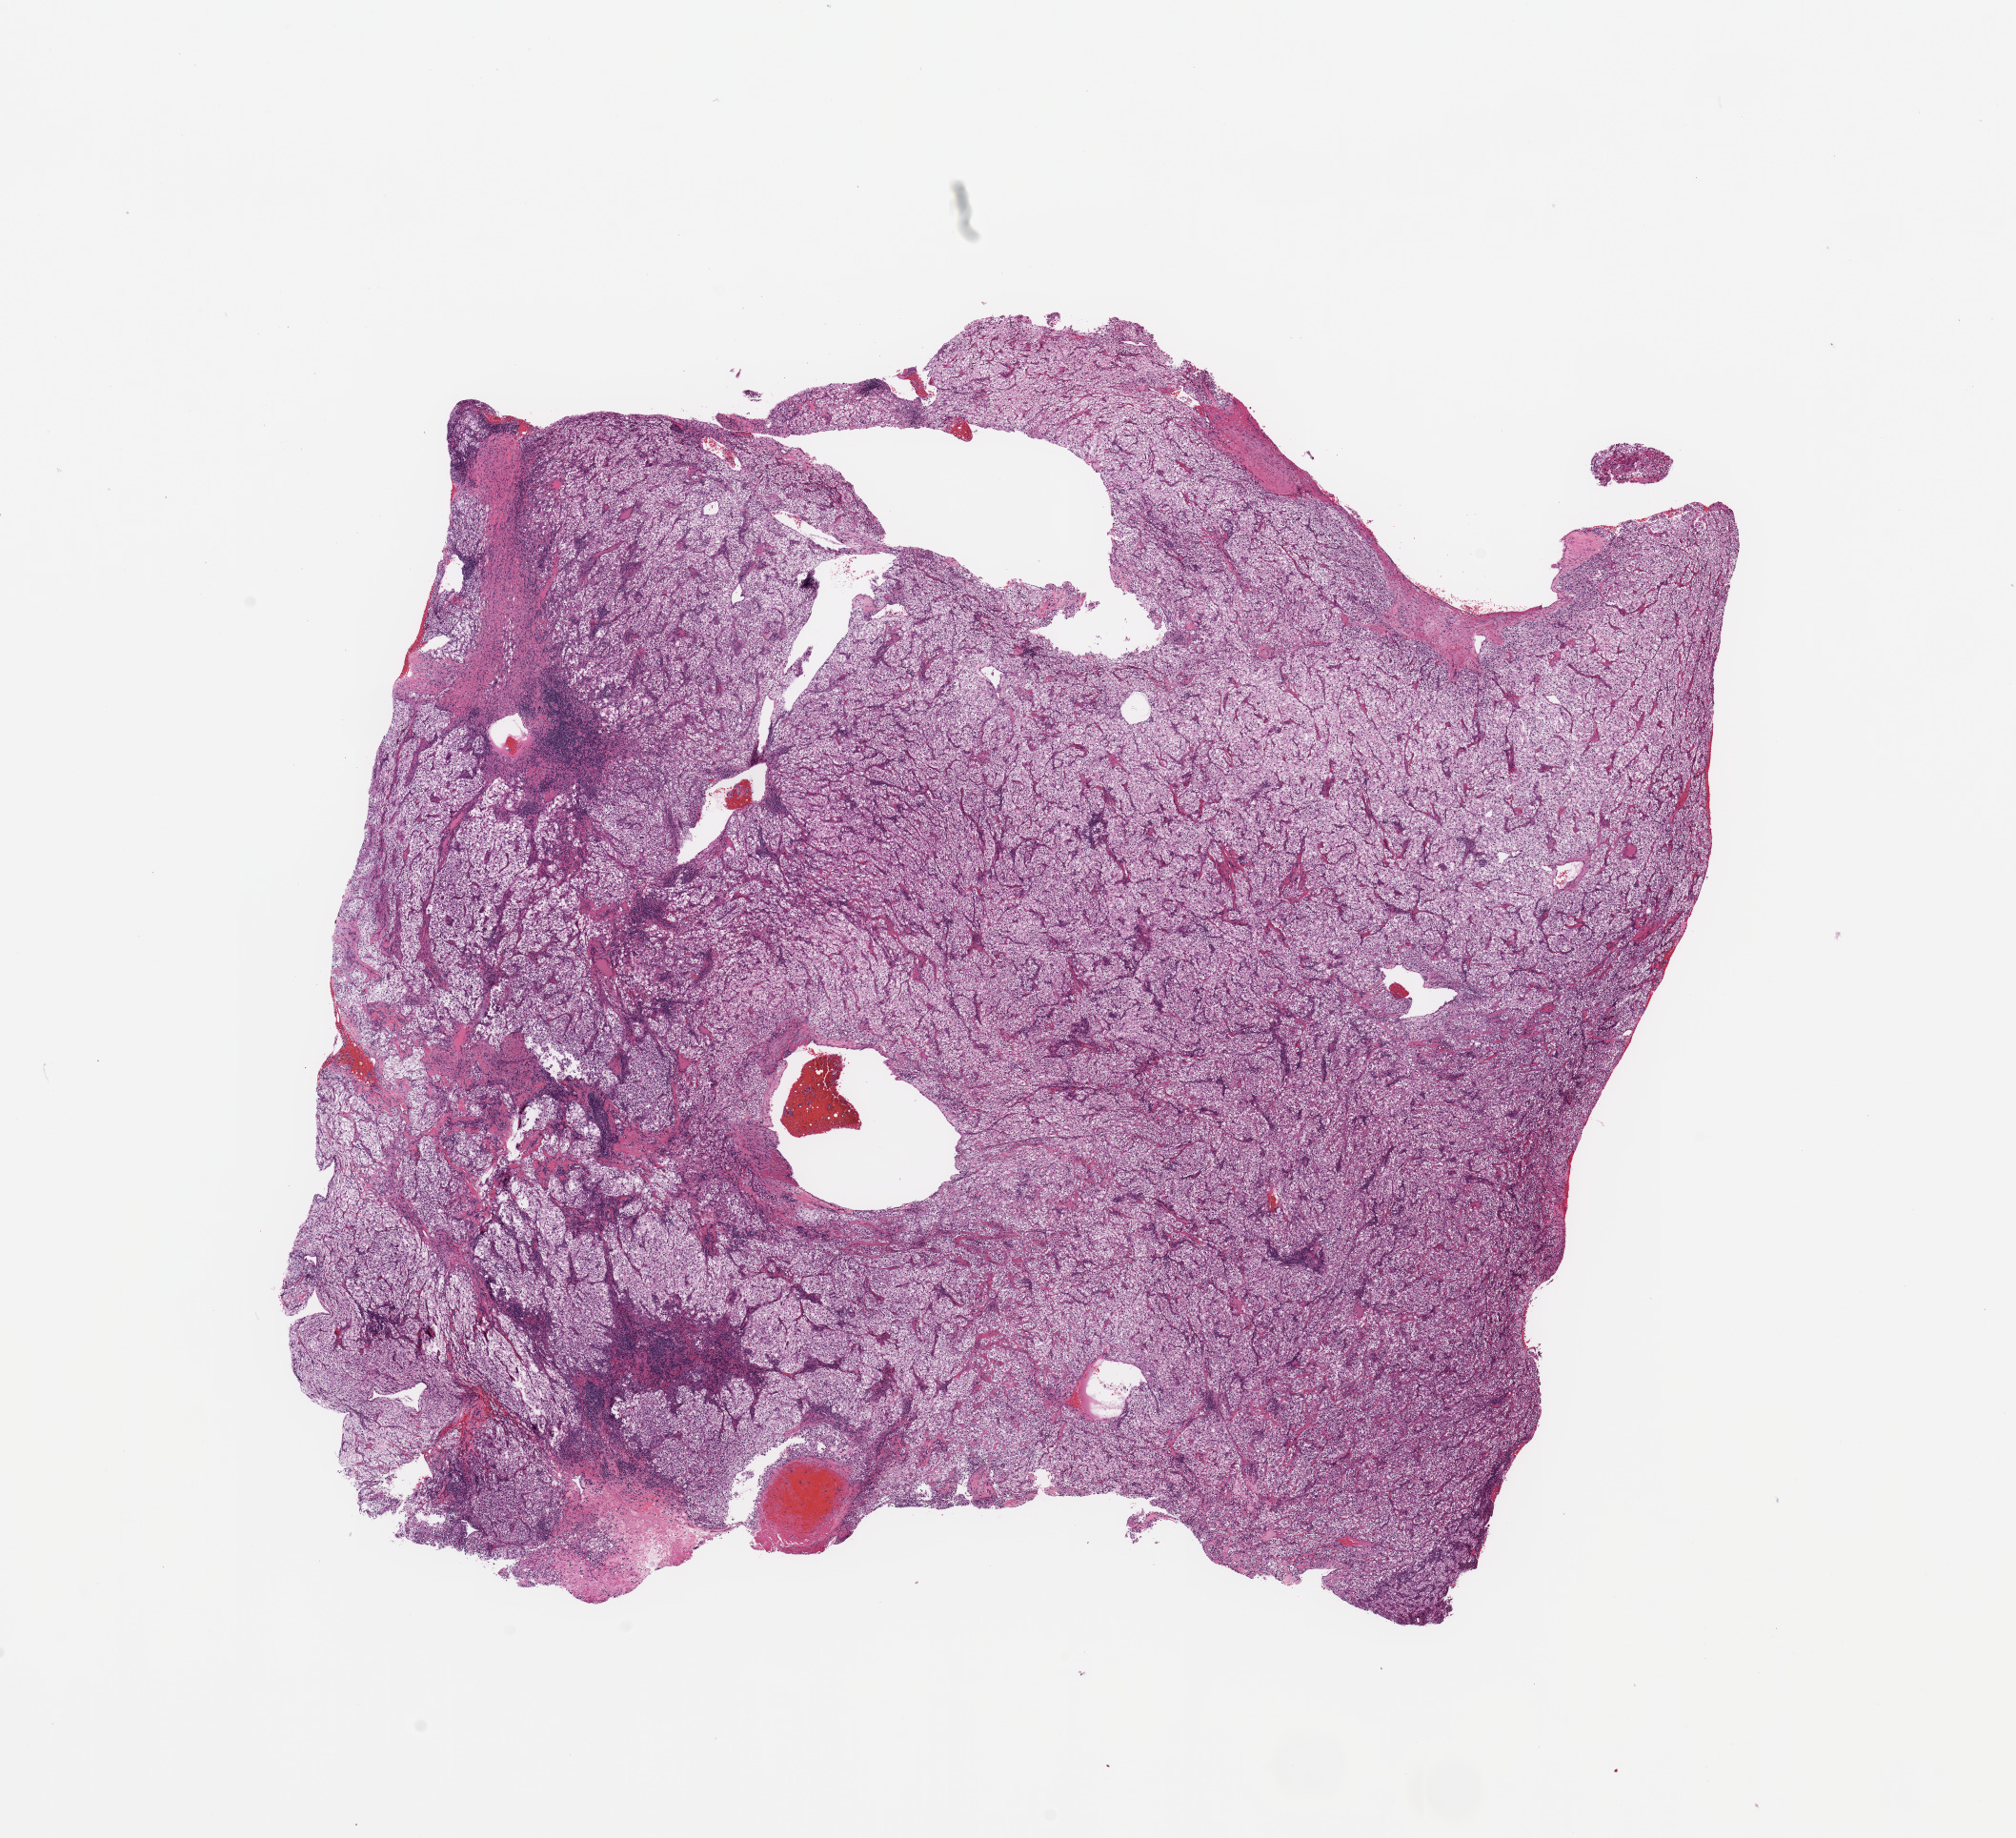
Whole-slide histology image, Hematoxylin and eosin (H&E) stained, low-resolution overview of the scanned area, about 16.7 x 15.3 mm. Tumour tissue sample, kidney. Male, 40 y/o. Histologic grade: G3 (poorly differentiated).
Diagnosis: Renal cell carcinoma, NOS. AJCC pathologic stage: IV.